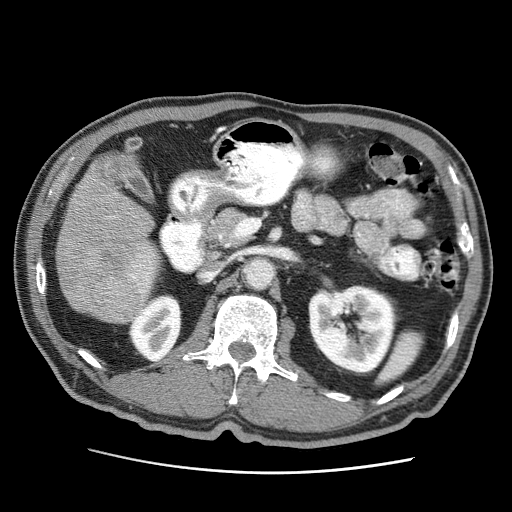
Contrast-enhanced abdominal CT (liver protocol), one axial slice. Slice 14 of 75 in the series (ordered by position). Reconstruction kernel STANDARD. Soft-tissue window (W 400 / L 40 HU). 512 × 512 image matrix. Case-level facts recorded for this patient, not image findings: diagnosis: hepatocellular carcinoma (patient treated with transarterial chemoembolisation; whether this scan precedes or follows treatment is not stated here); TNM stage (as recorded): Stage-IIIA; Child-Pugh class: A.
Outlined on this slice (semi-automatic segmentation, software-assisted and operator-edited):
- liver parenchyma outside the tumour (the mass and vessels are separate outlines, so this box may not span the whole liver): bounding box [x1, y1, x2, y2] px = [56, 158, 158, 324]
- mass: [57, 159, 146, 309]
- liver vessels: [130, 255, 152, 293]